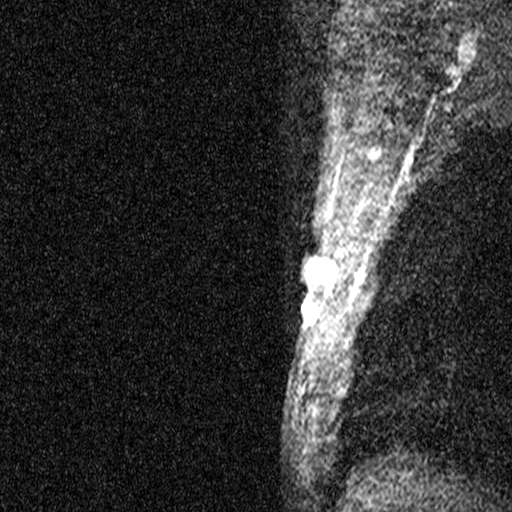
Breast MRI (dynamic contrast-enhanced), one sagittal slice. Position 36 of 44 along the scan axis. Dynamic contrast-enhanced study with each time point stored as its own series, time point 2 of 3 at this slice position (early post-contrast, ordered by acquisition time). 1.5 T. TE 4.5 ms, TR 11 ms. 512 × 512 image matrix, field of view 200 × 200 mm. Female patient, age 45 years. Case-level facts recorded for this patient, not image findings: setting: breast cancer imaged before/during neoadjuvant chemotherapy; receptor status: HR-positive, HER2-negative.
Structures marked on this image (semi-automatically segmented with operator editing):
- analysis volume of interest (the breast-tissue region the enhancement analysis was run in; not a lesion): box from (x=256, y=218) to (x=343, y=359) px
- tumour enhancement mask (voxels above the 90 % enhancement threshold inside the analysis volume of interest): (x=304, y=262)–(x=336, y=309)